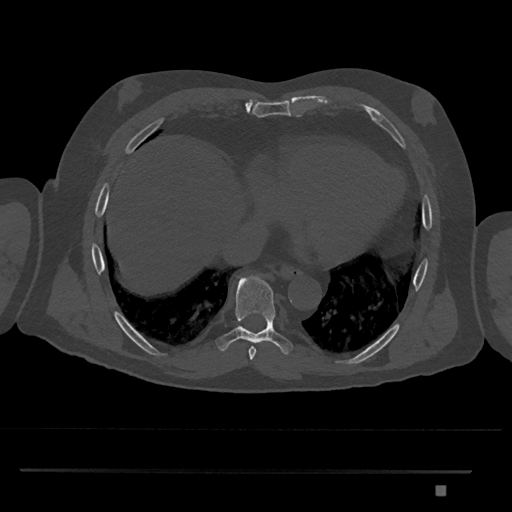
CT including the spine, one axial slice. Position 1115 of 1134 along the scan axis. Reconstruction kernel Br40s/3. Bone window (W 1800 / L 400 HU). 0.5 mm slice thickness. 512 × 512 image matrix, field of view 429 × 429 mm. Male patient, age 65 years. Case-level facts recorded for this patient, not image findings: primary cancer: prostate.
Annotated regions visible in this slice (semi-automatically segmented with operator editing):
- T8 vertebra: box from (x=216, y=275) to (x=293, y=354) px